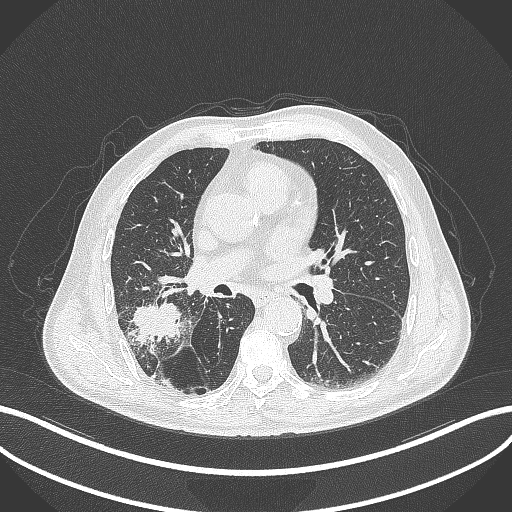
Chest CT, one axial slice. Lung window (W 1500 / L -600 HU). 1 mm slice thickness. 512 × 512 image matrix. Patient: male, 72 years. Case-level facts recorded for this patient, not image findings: clinical TNM (as recorded): T3 N2 M0.
Annotated regions visible in this slice (bounding box drawn by a radiologist):
- lung tumour (recorded histology: adenocarcinoma): bounding box <128,303,187,347> (left, top, right, bottom; pixels)